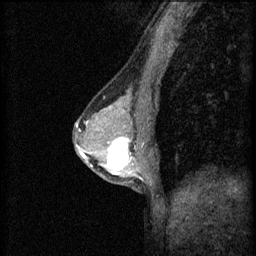
Breast MRI (dynamic contrast-enhanced), one sagittal slice. 3 images stored at this slice position (order not interpretable as contrast timing). 1.5 T. TE 4.2 ms, TR 8.2 ms. 256 × 256 image matrix, field of view 180 × 180 mm. Patient: female, 44 years.
Outlined on this slice (semi-automatically segmented with operator editing):
- analysis volume of interest (the breast-tissue region the enhancement analysis was run in; not a lesion): bounding box <102,132,151,181> (left, top, right, bottom; pixels)
- tumour enhancement mask (voxels above the 70 % enhancement threshold inside the analysis volume of interest): <106,138,137,177>